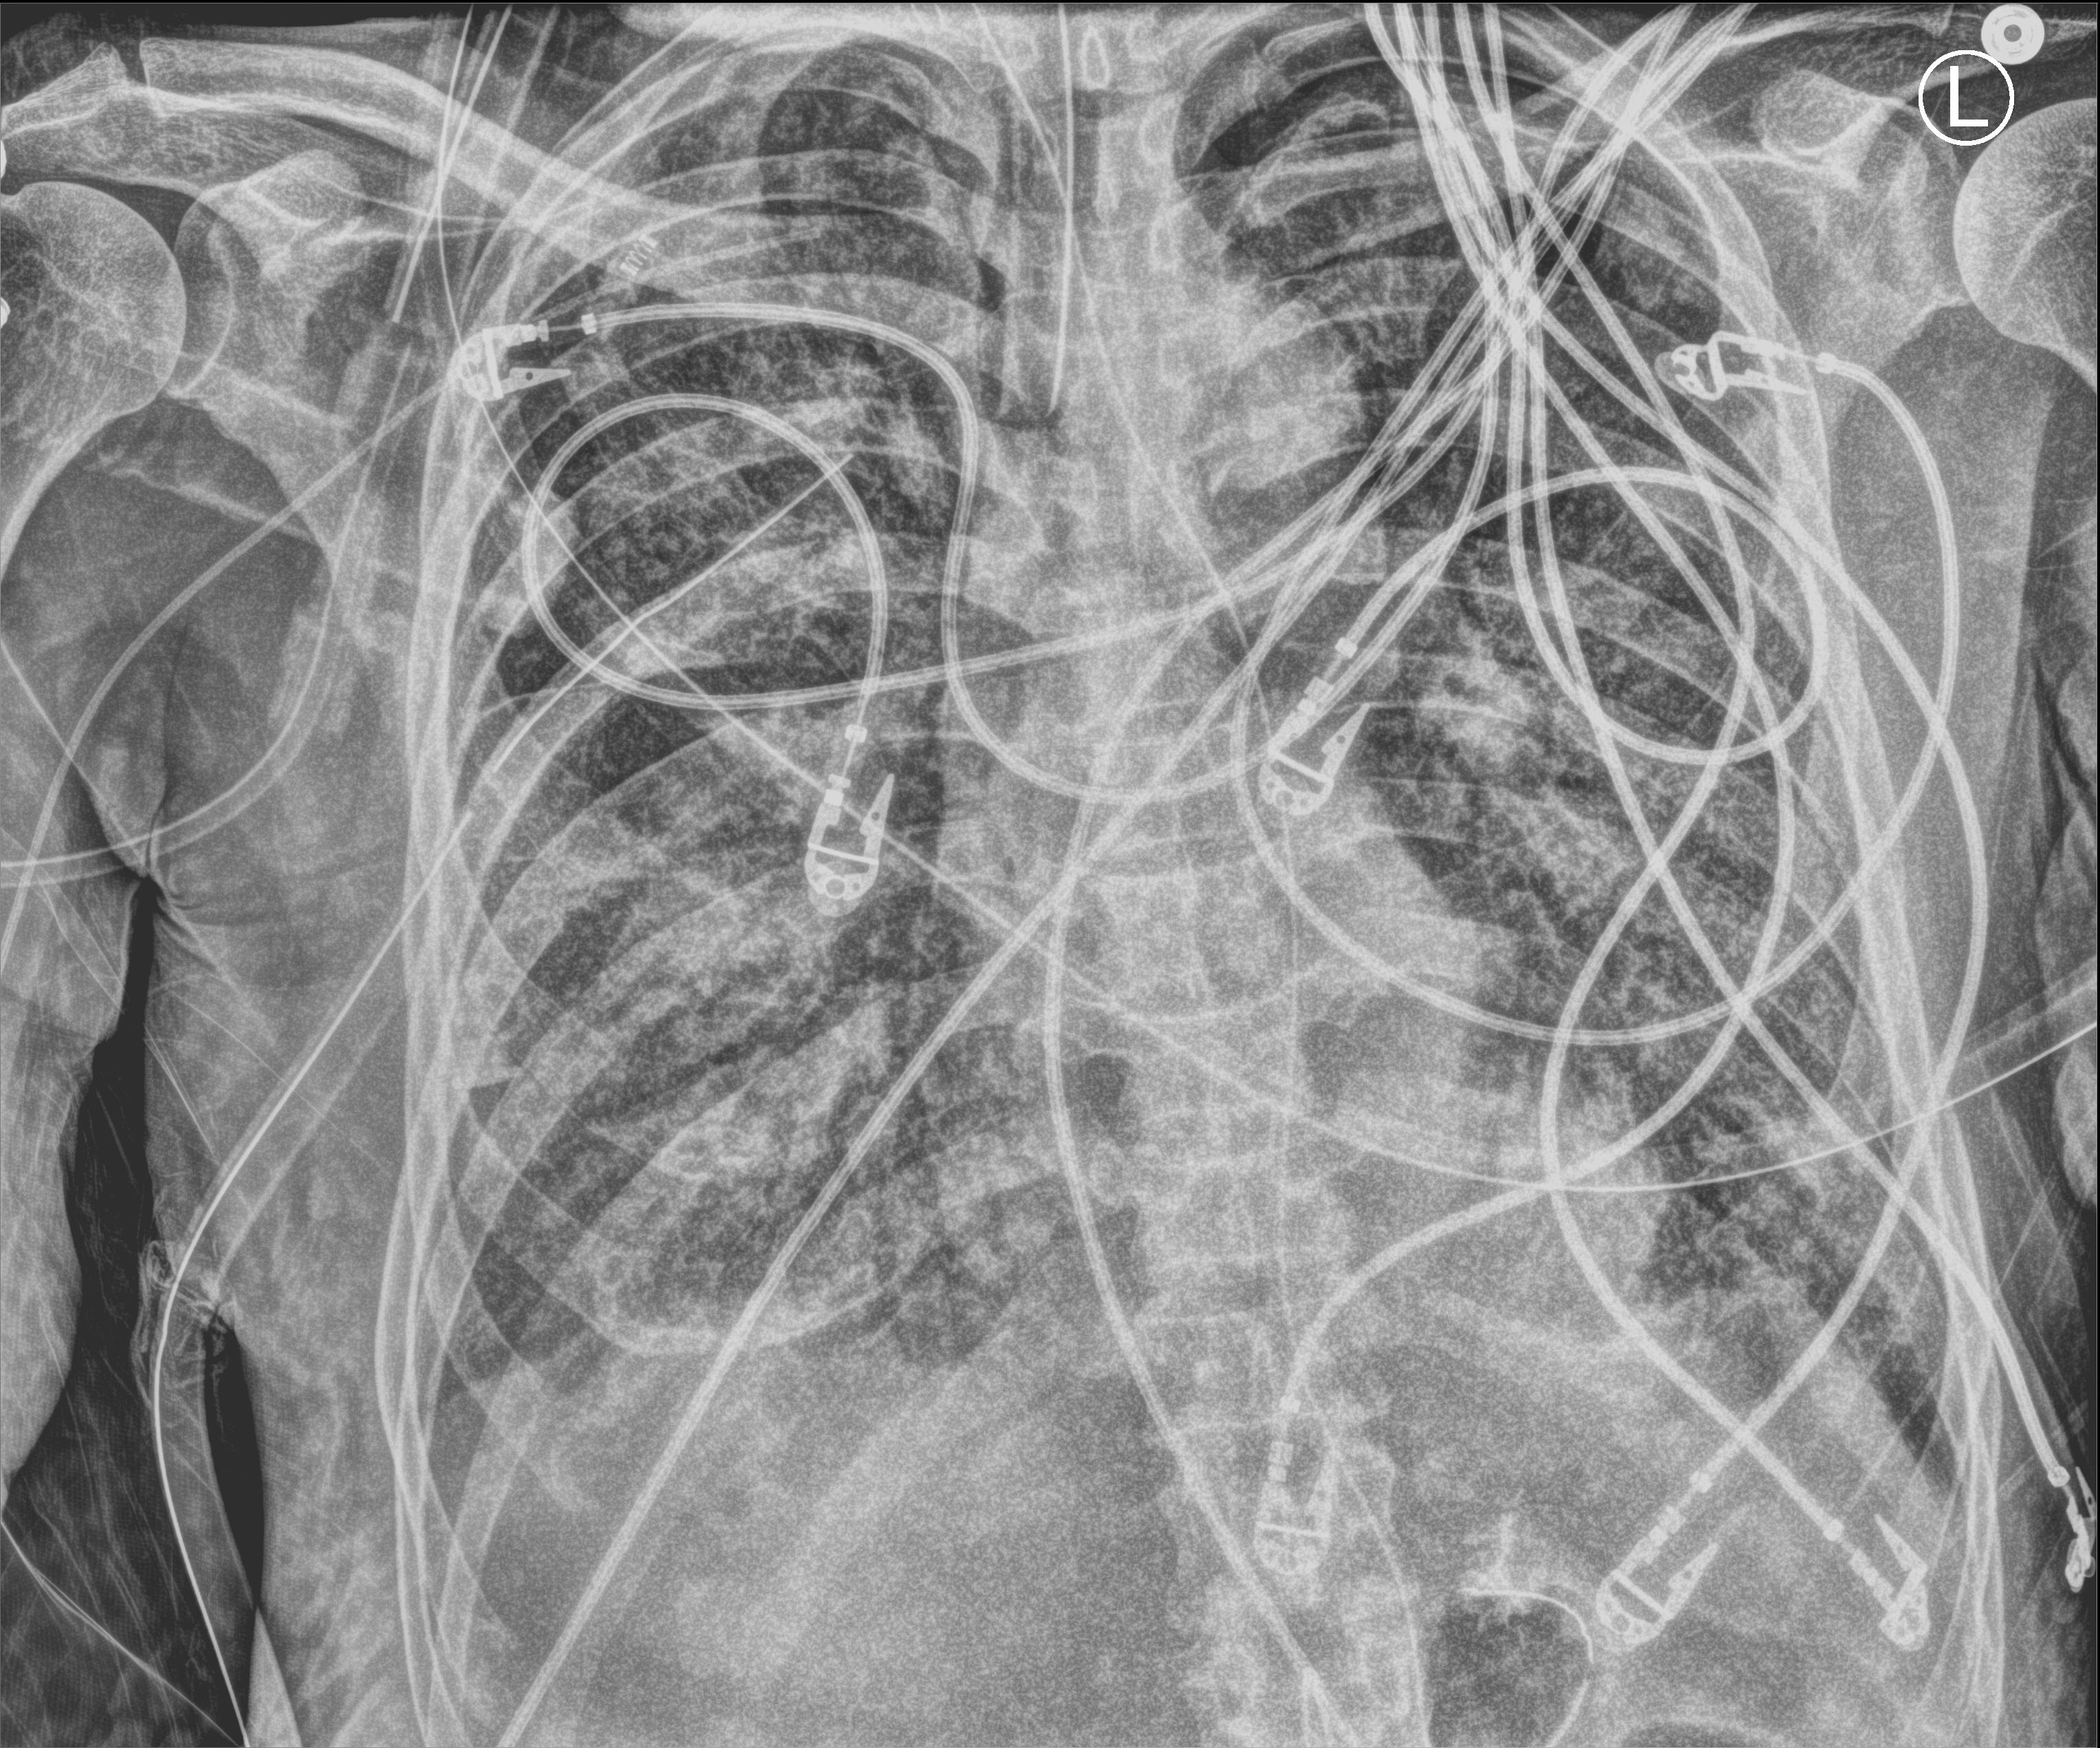
Bedside chest radiograph (computed radiography); anteroposterior (AP) projection. Patient hospitalised with COVID-19; male, aged 60–74 years.
From the hospital-stay record, not from the radiograph (when in the stay this image was taken is not recorded): admitted to intensive care during this hospital stay: yes.